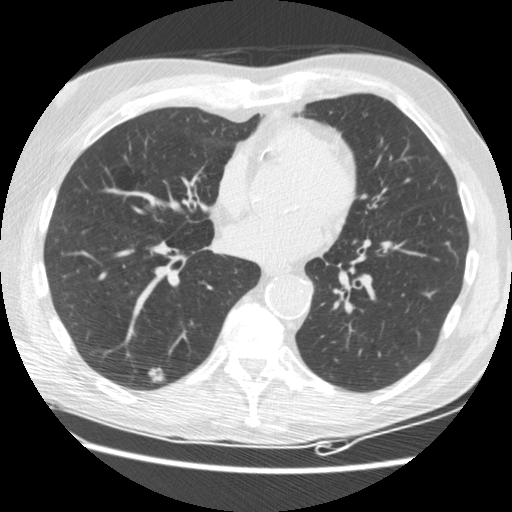
Low-dose screening chest CT, one axial slice; position 78 of 176 along the scan axis; 120 kVp; lung window (W 1500 / L -600 HU); 512 × 512 image matrix.
Outlined on this slice (manually delineated by an expert):
- lesion 2 (tumor, lower lobe of right lung): bounding box (x1, y1, x2, y2) in pixels: (149, 368, 166, 383)